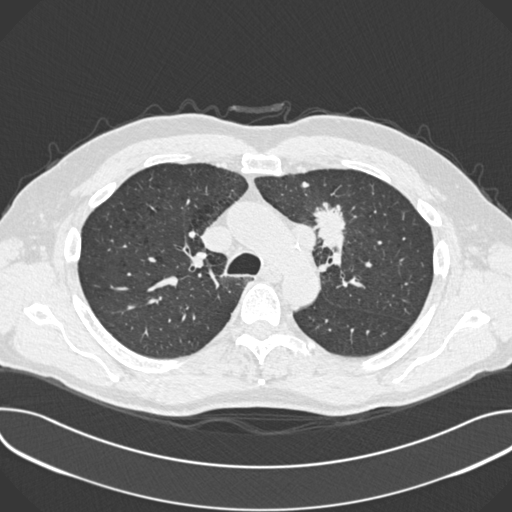
Low-dose screening chest CT, one axial slice; 120 kVp; lung window (W 1500 / L -600 HU); 1 mm slice thickness; 512 × 512 image matrix, field of view 380 × 380 mm.
Structures marked on this image (expert manual segmentation):
- lesion 1 (tumor, upper lobe of left lung): bounding box <314,207,345,248> (left, top, right, bottom; pixels)